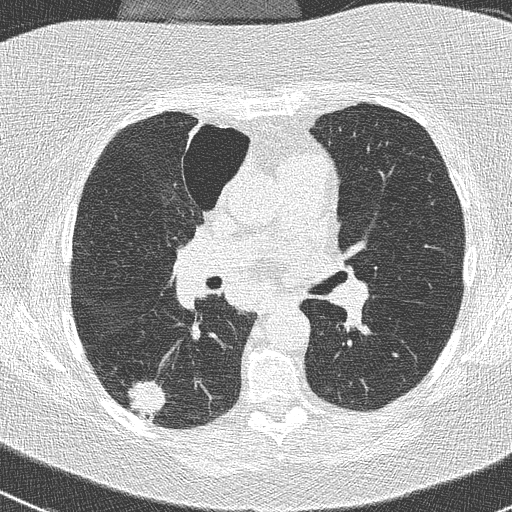
Low-dose screening chest CT, one axial slice. Slice 146 of 261 in the series (ordered by position). Lung window (W 1500 / L -600 HU). 2 mm slice thickness. 512 × 512 image matrix, field of view 310 × 310 mm.
Outlined on this slice (outlined manually by an expert reader):
- lesion 1 (tumor, lower lobe of right lung): bounding box [x1, y1, x2, y2] px = [128, 380, 166, 420]